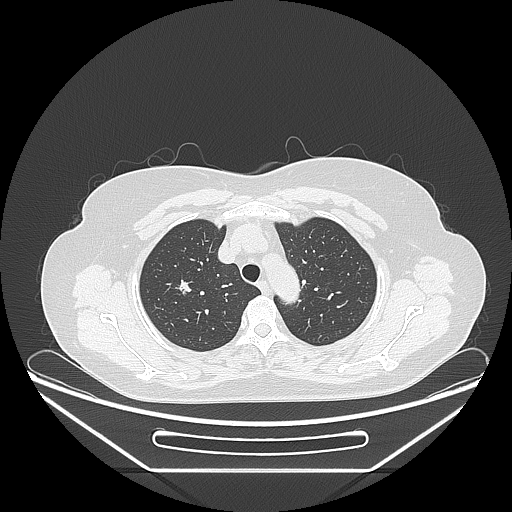
Chest CT, one axial slice; position 195 of 236 along the scan axis; reconstruction kernel LUNG; lung window (W 1500 / L -600 HU); 1.25 mm slice thickness; 512 × 512 image matrix, field of view 433 × 433 mm. Female patient, age 60 years. Case-level facts recorded for this patient, not image findings: clinical TNM (as recorded): T1c N0 M0; histopathological grade: G2-3.
Outlined on this slice (rectangle marked by the reading radiologist):
- lung tumour (recorded histology: adenocarcinoma): bounding box [x1, y1, x2, y2] px = [174, 274, 198, 303]